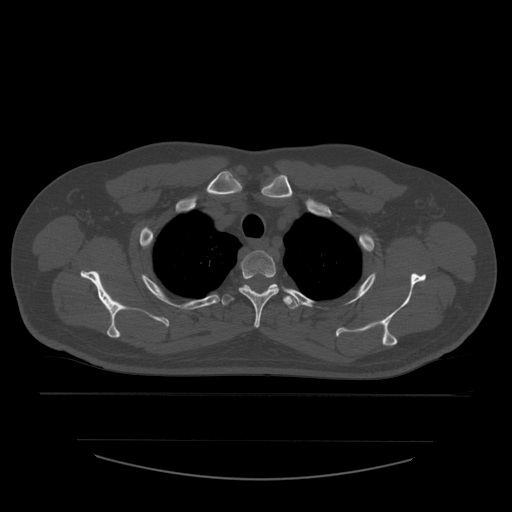
CT including the spine, one axial slice; position 447 of 532 along the scan axis; reconstruction kernel STANDARD; 120 kVp; bone window (W 1800 / L 400 HU); 1.25 mm slice thickness; 512 × 512 image matrix, field of view 441 × 441 mm. Patient age 44 years. From the clinical record (not read from this slice): primary cancer: soft tissue sarcoma.
Outlined on this slice (semi-automatically segmented with operator editing):
- T2 vertebra: bounding box [x1, y1, x2, y2] px = [239, 251, 280, 328]
- T3 vertebra: [222, 284, 299, 309]